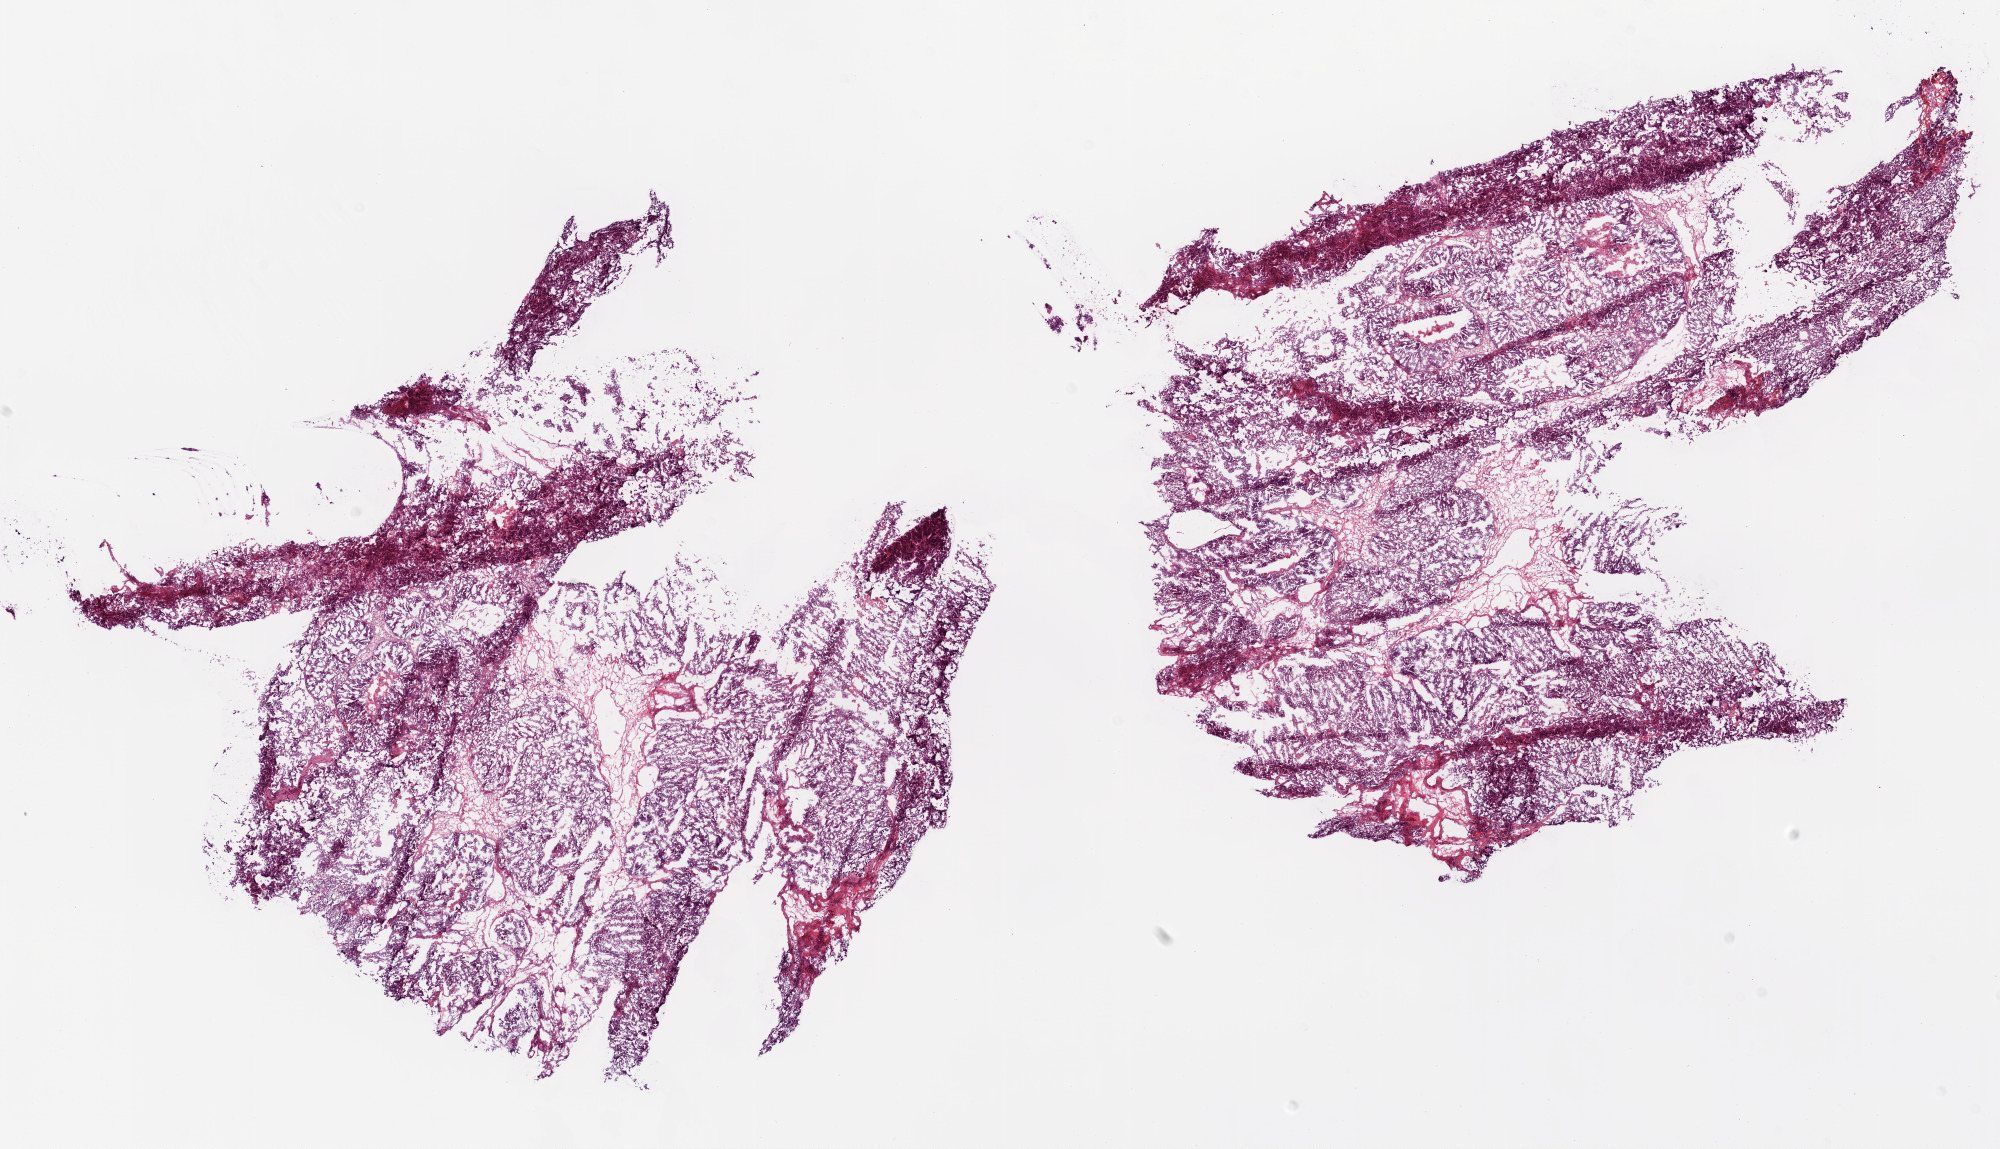
Digitized H&E tissue section (whole slide), a low-resolution overview of the entire scanned area, about 16.0 x 9.2 mm. Frozen section from the top of the tissue portion. Primary tumour sample from the ovary. Female, age 53 years at initial diagnosis. Histologic grade: G3 (poorly differentiated). Pathologist review of this section (percent, as recorded): tumour cells 90%, tumour nuclei 90%, normal cells 0%, stromal cells 8%, necrosis 2%.
Laterality: bilateral. FIGO stage: IIIC. Histologic diagnosis: Serous cystadenocarcinoma, NOS.